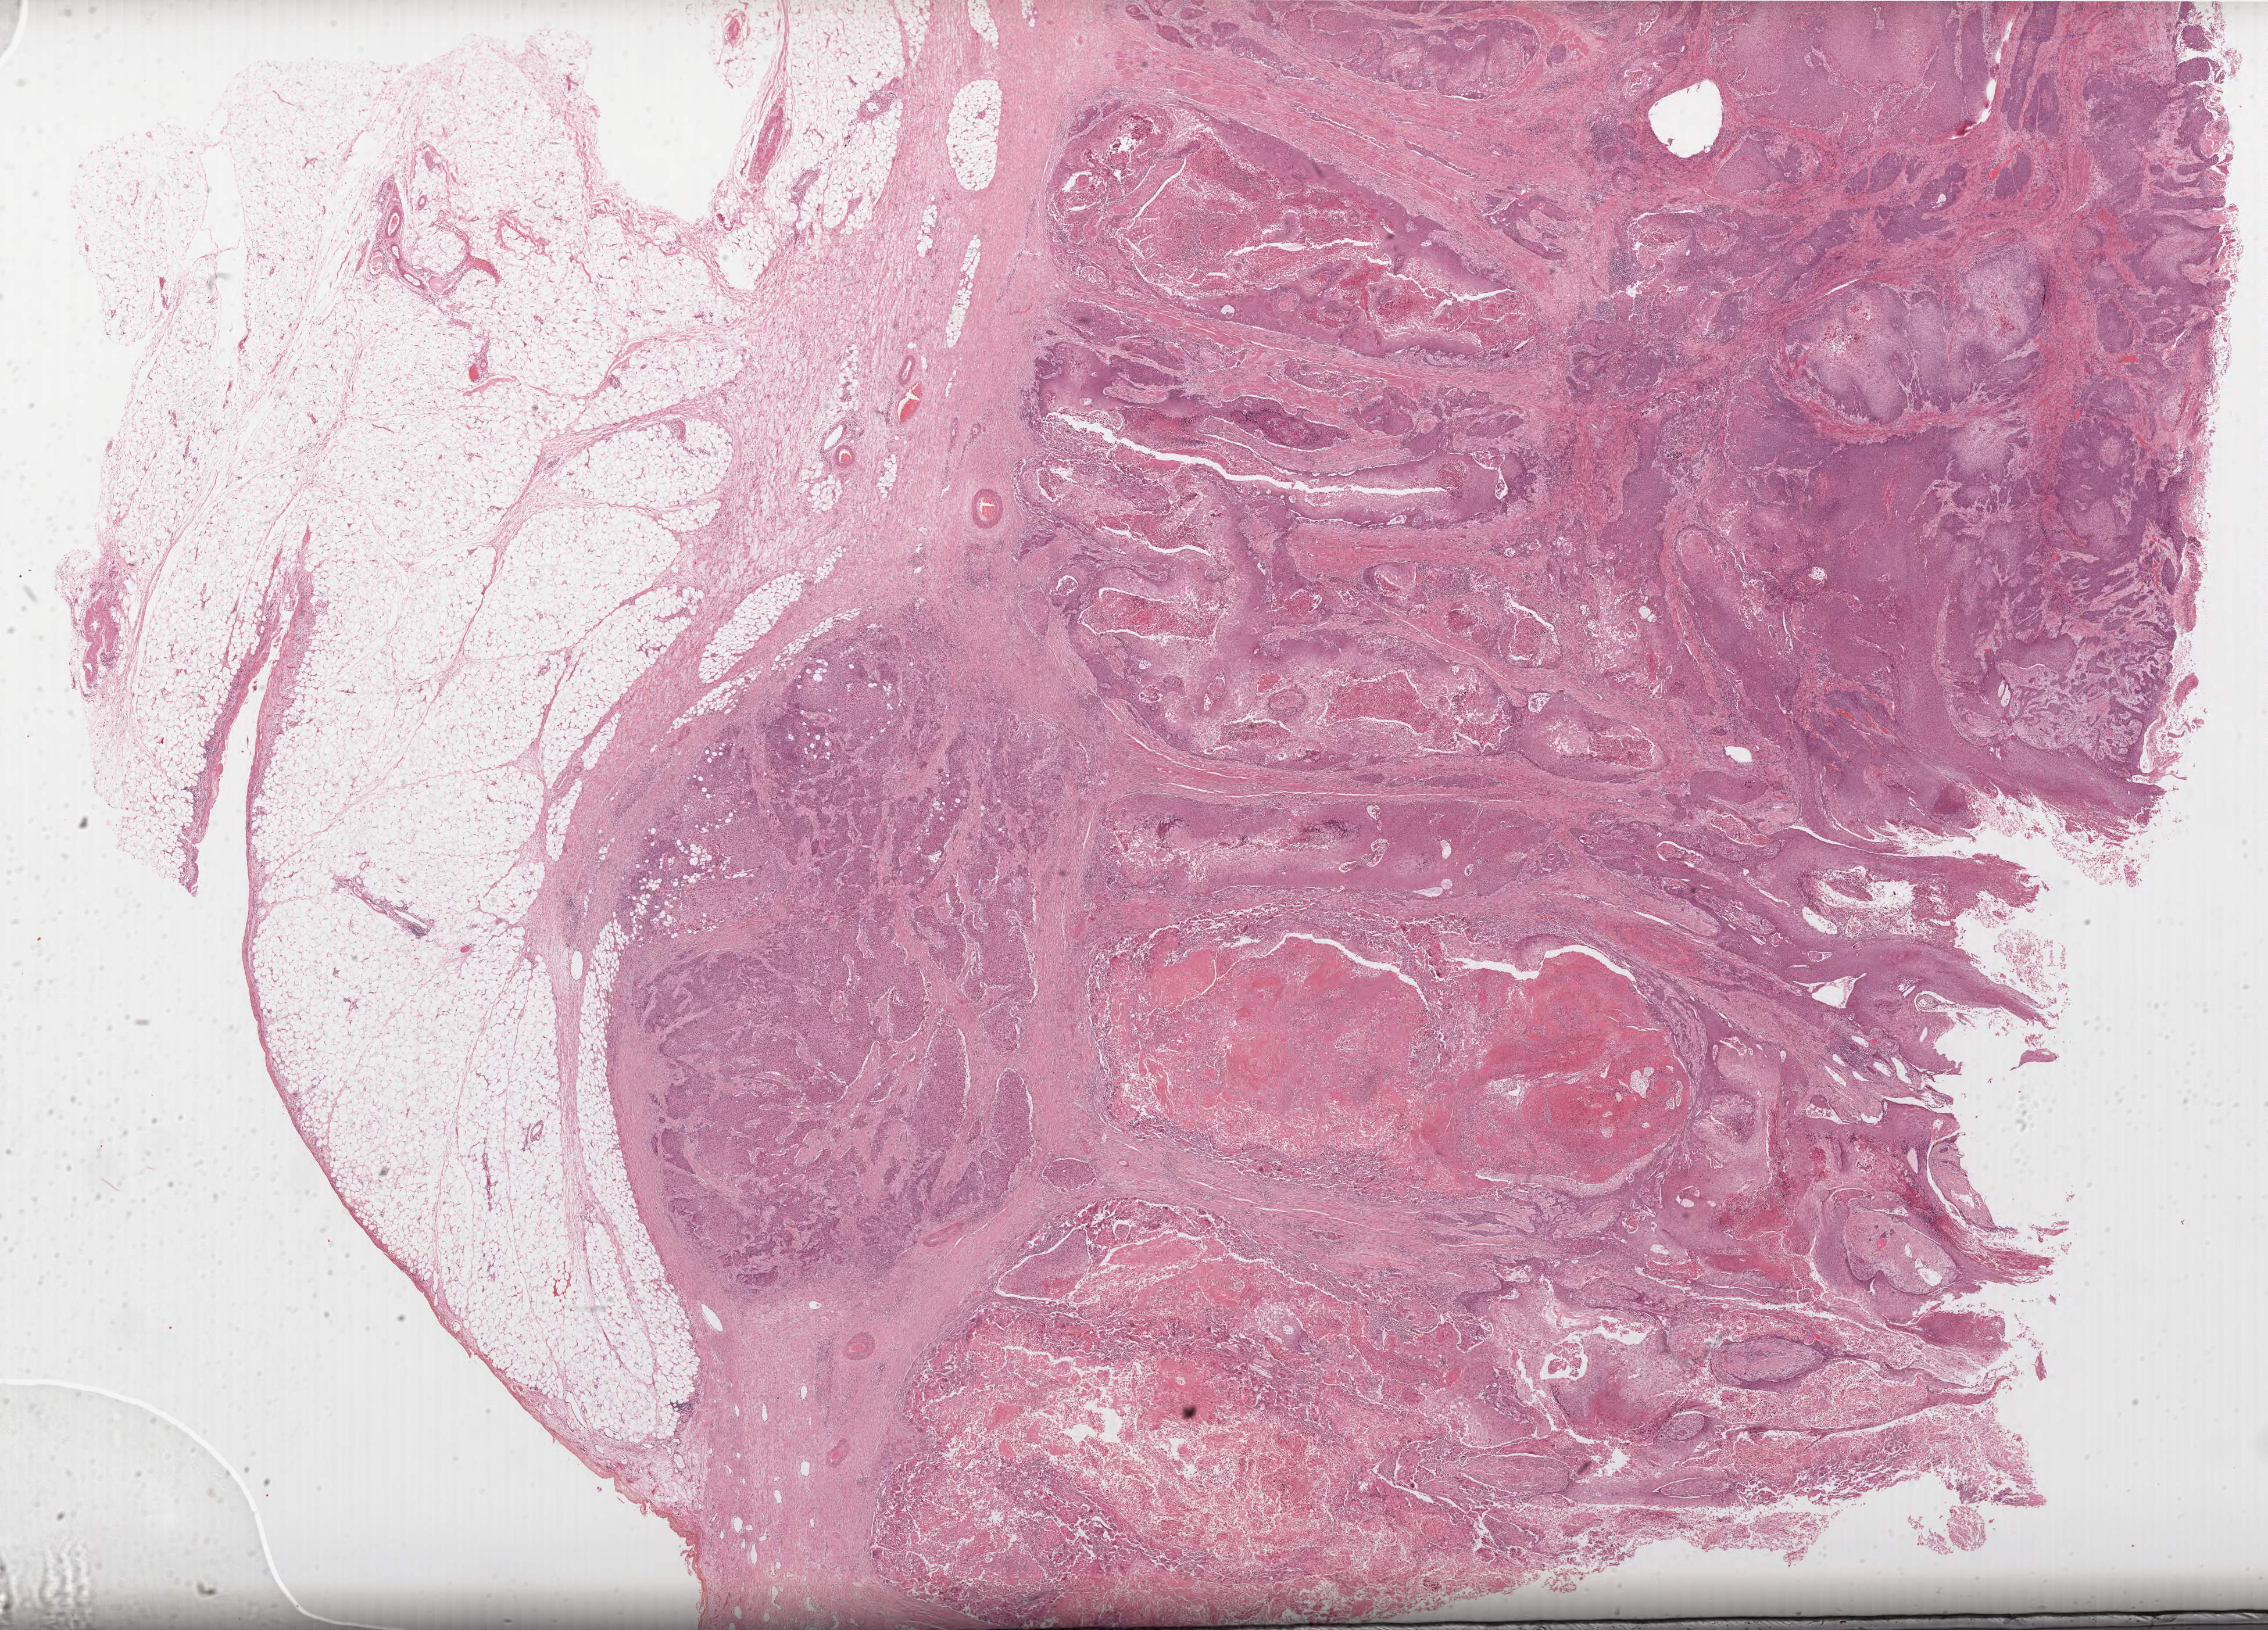
H&E whole-slide image — low-resolution overview of the scanned area, about 31.4 x 22.6 mm. Formalin-fixed paraffin-embedded (FFPE) diagnostic section. Sample: primary tumour, esophagus. Male patient; age at initial diagnosis 50 years.
Pathologic diagnosis: Squamous cell carcinoma, NOS.